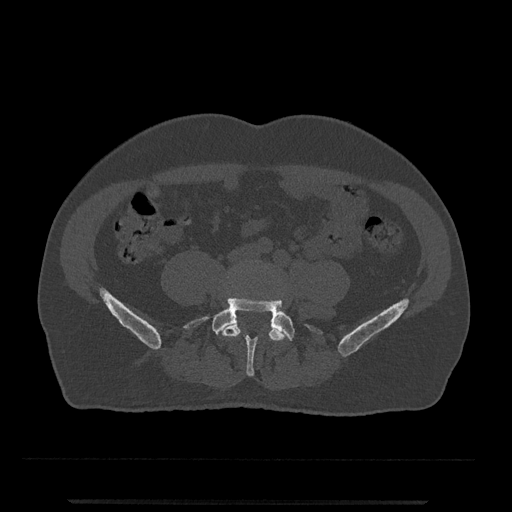
CT including the spine, one axial slice; slice 93 of 797 in the series (ordered by position); reconstruction kernel Br40s/3; bone window (W 1800 / L 400 HU); 0.5 mm slice thickness; 512 × 512 image matrix, field of view 419 × 419 mm. Patient: male, 63 years. From the clinical record (not read from this slice): primary cancer: prostate.
Annotated regions visible in this slice (semi-automatically segmented with operator editing):
- L4 vertebra: bounding box <222,319,288,361> (left, top, right, bottom; pixels)
- L5 vertebra: <184,297,322,376>